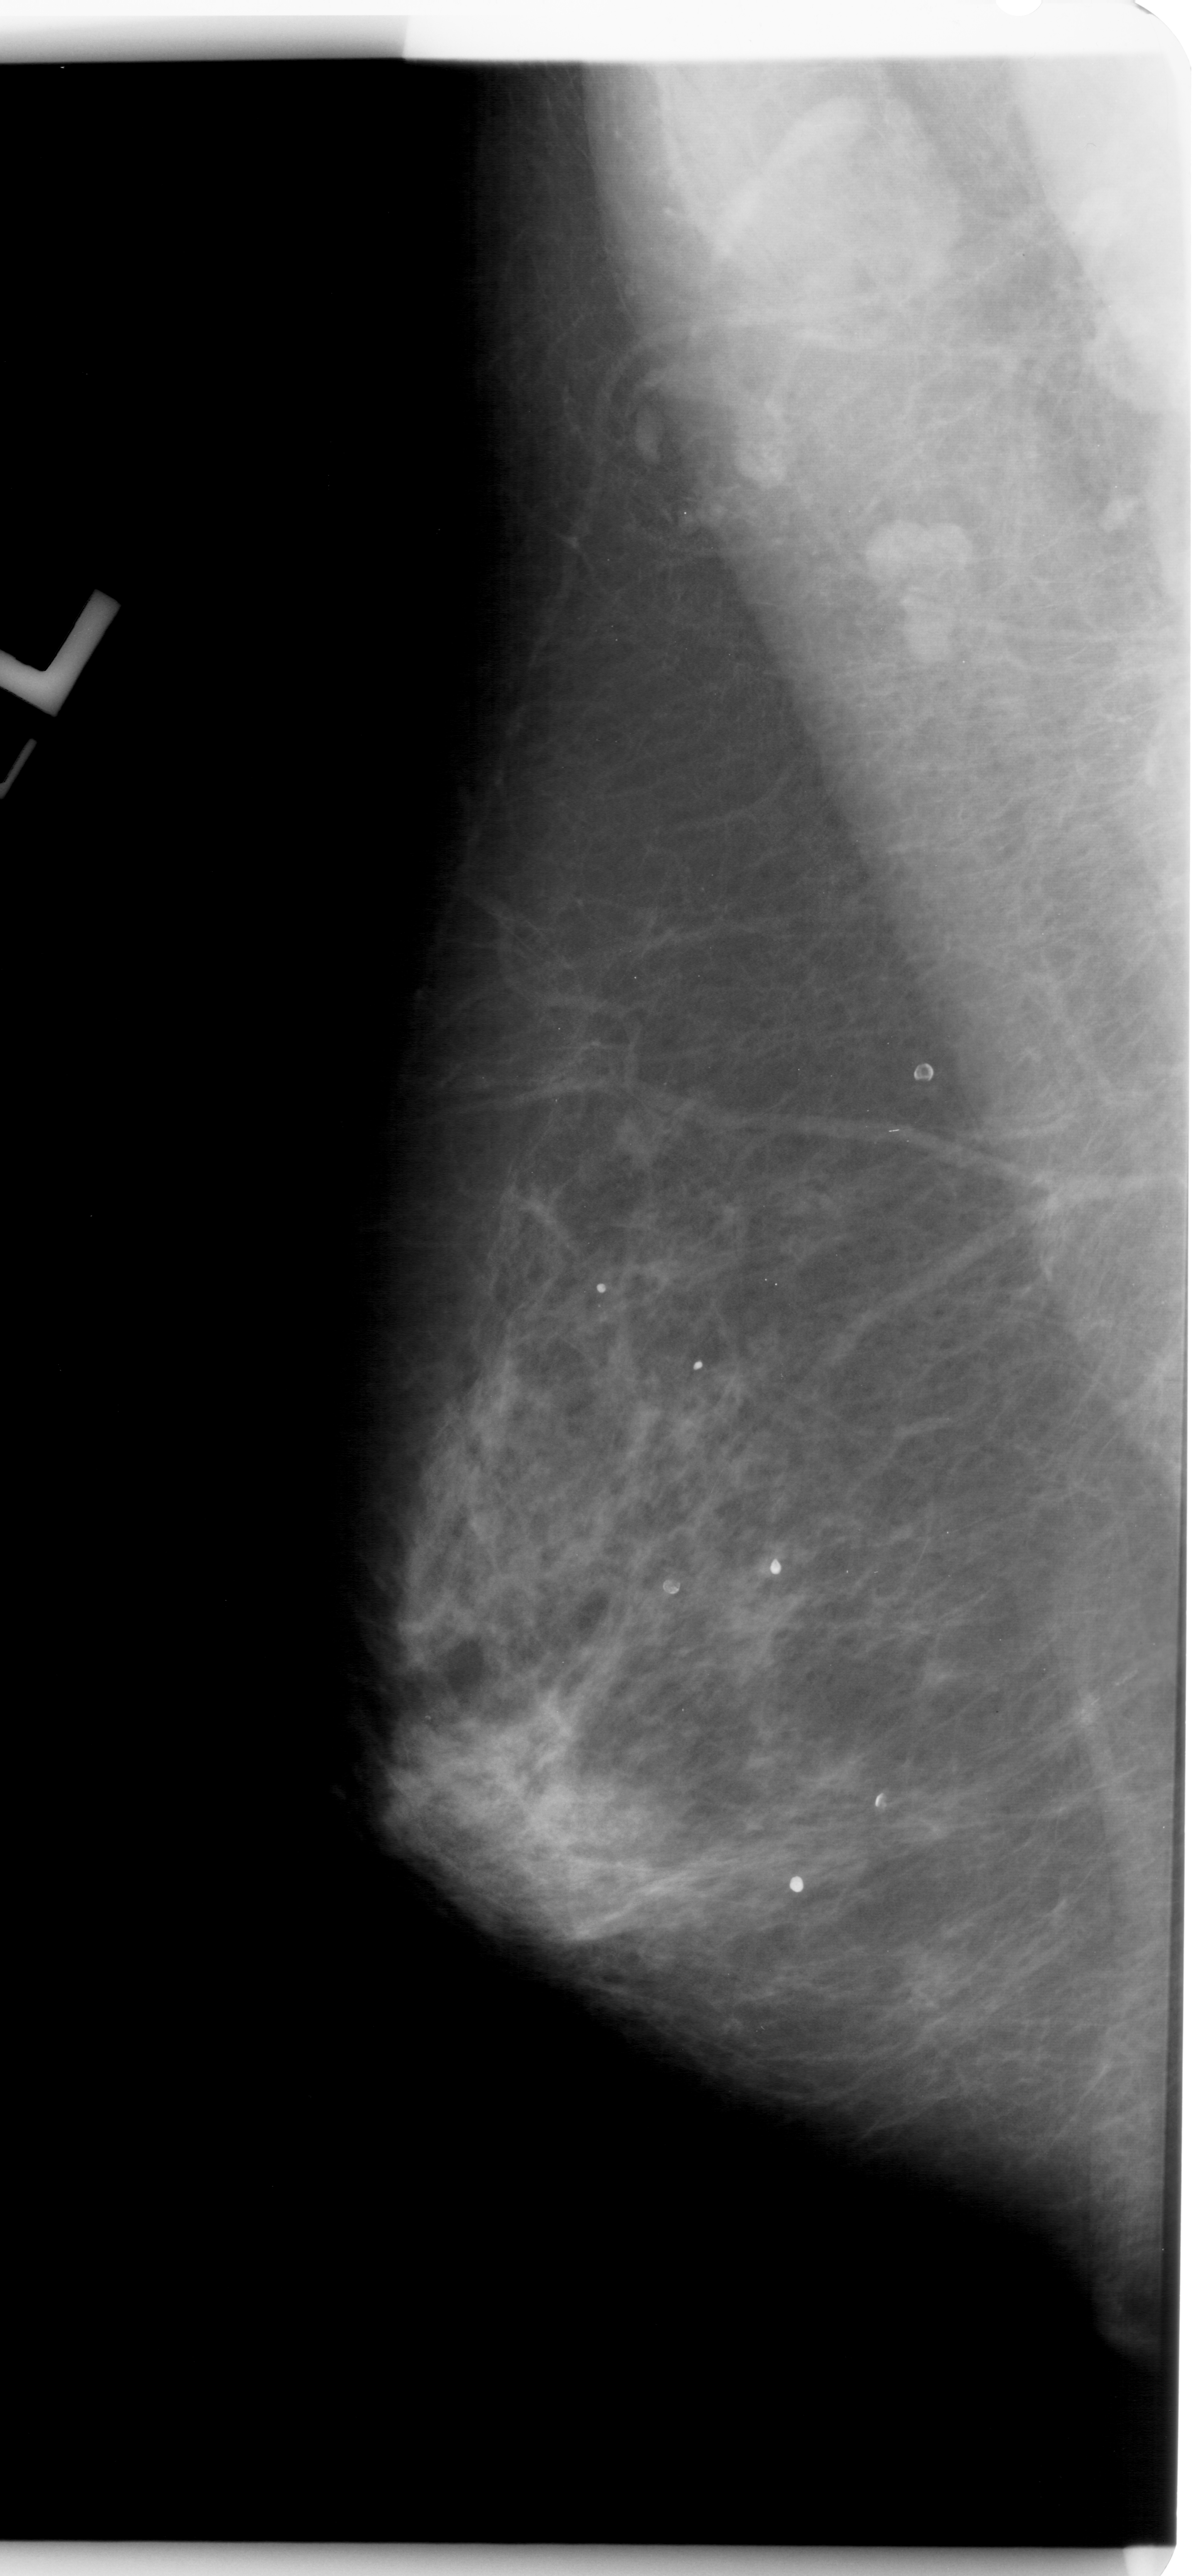
Mammogram (digitized film), left breast, MLO view, breast composition: heterogeneously dense (BI-RADS density category 3 of 4).
Marked findings (only marked abnormalities are described; nothing is implied about the rest of the image): mass, shape oval, margins ill defined; BI-RADS assessment category 4; pathology result (as recorded, not read from the image): malignant.